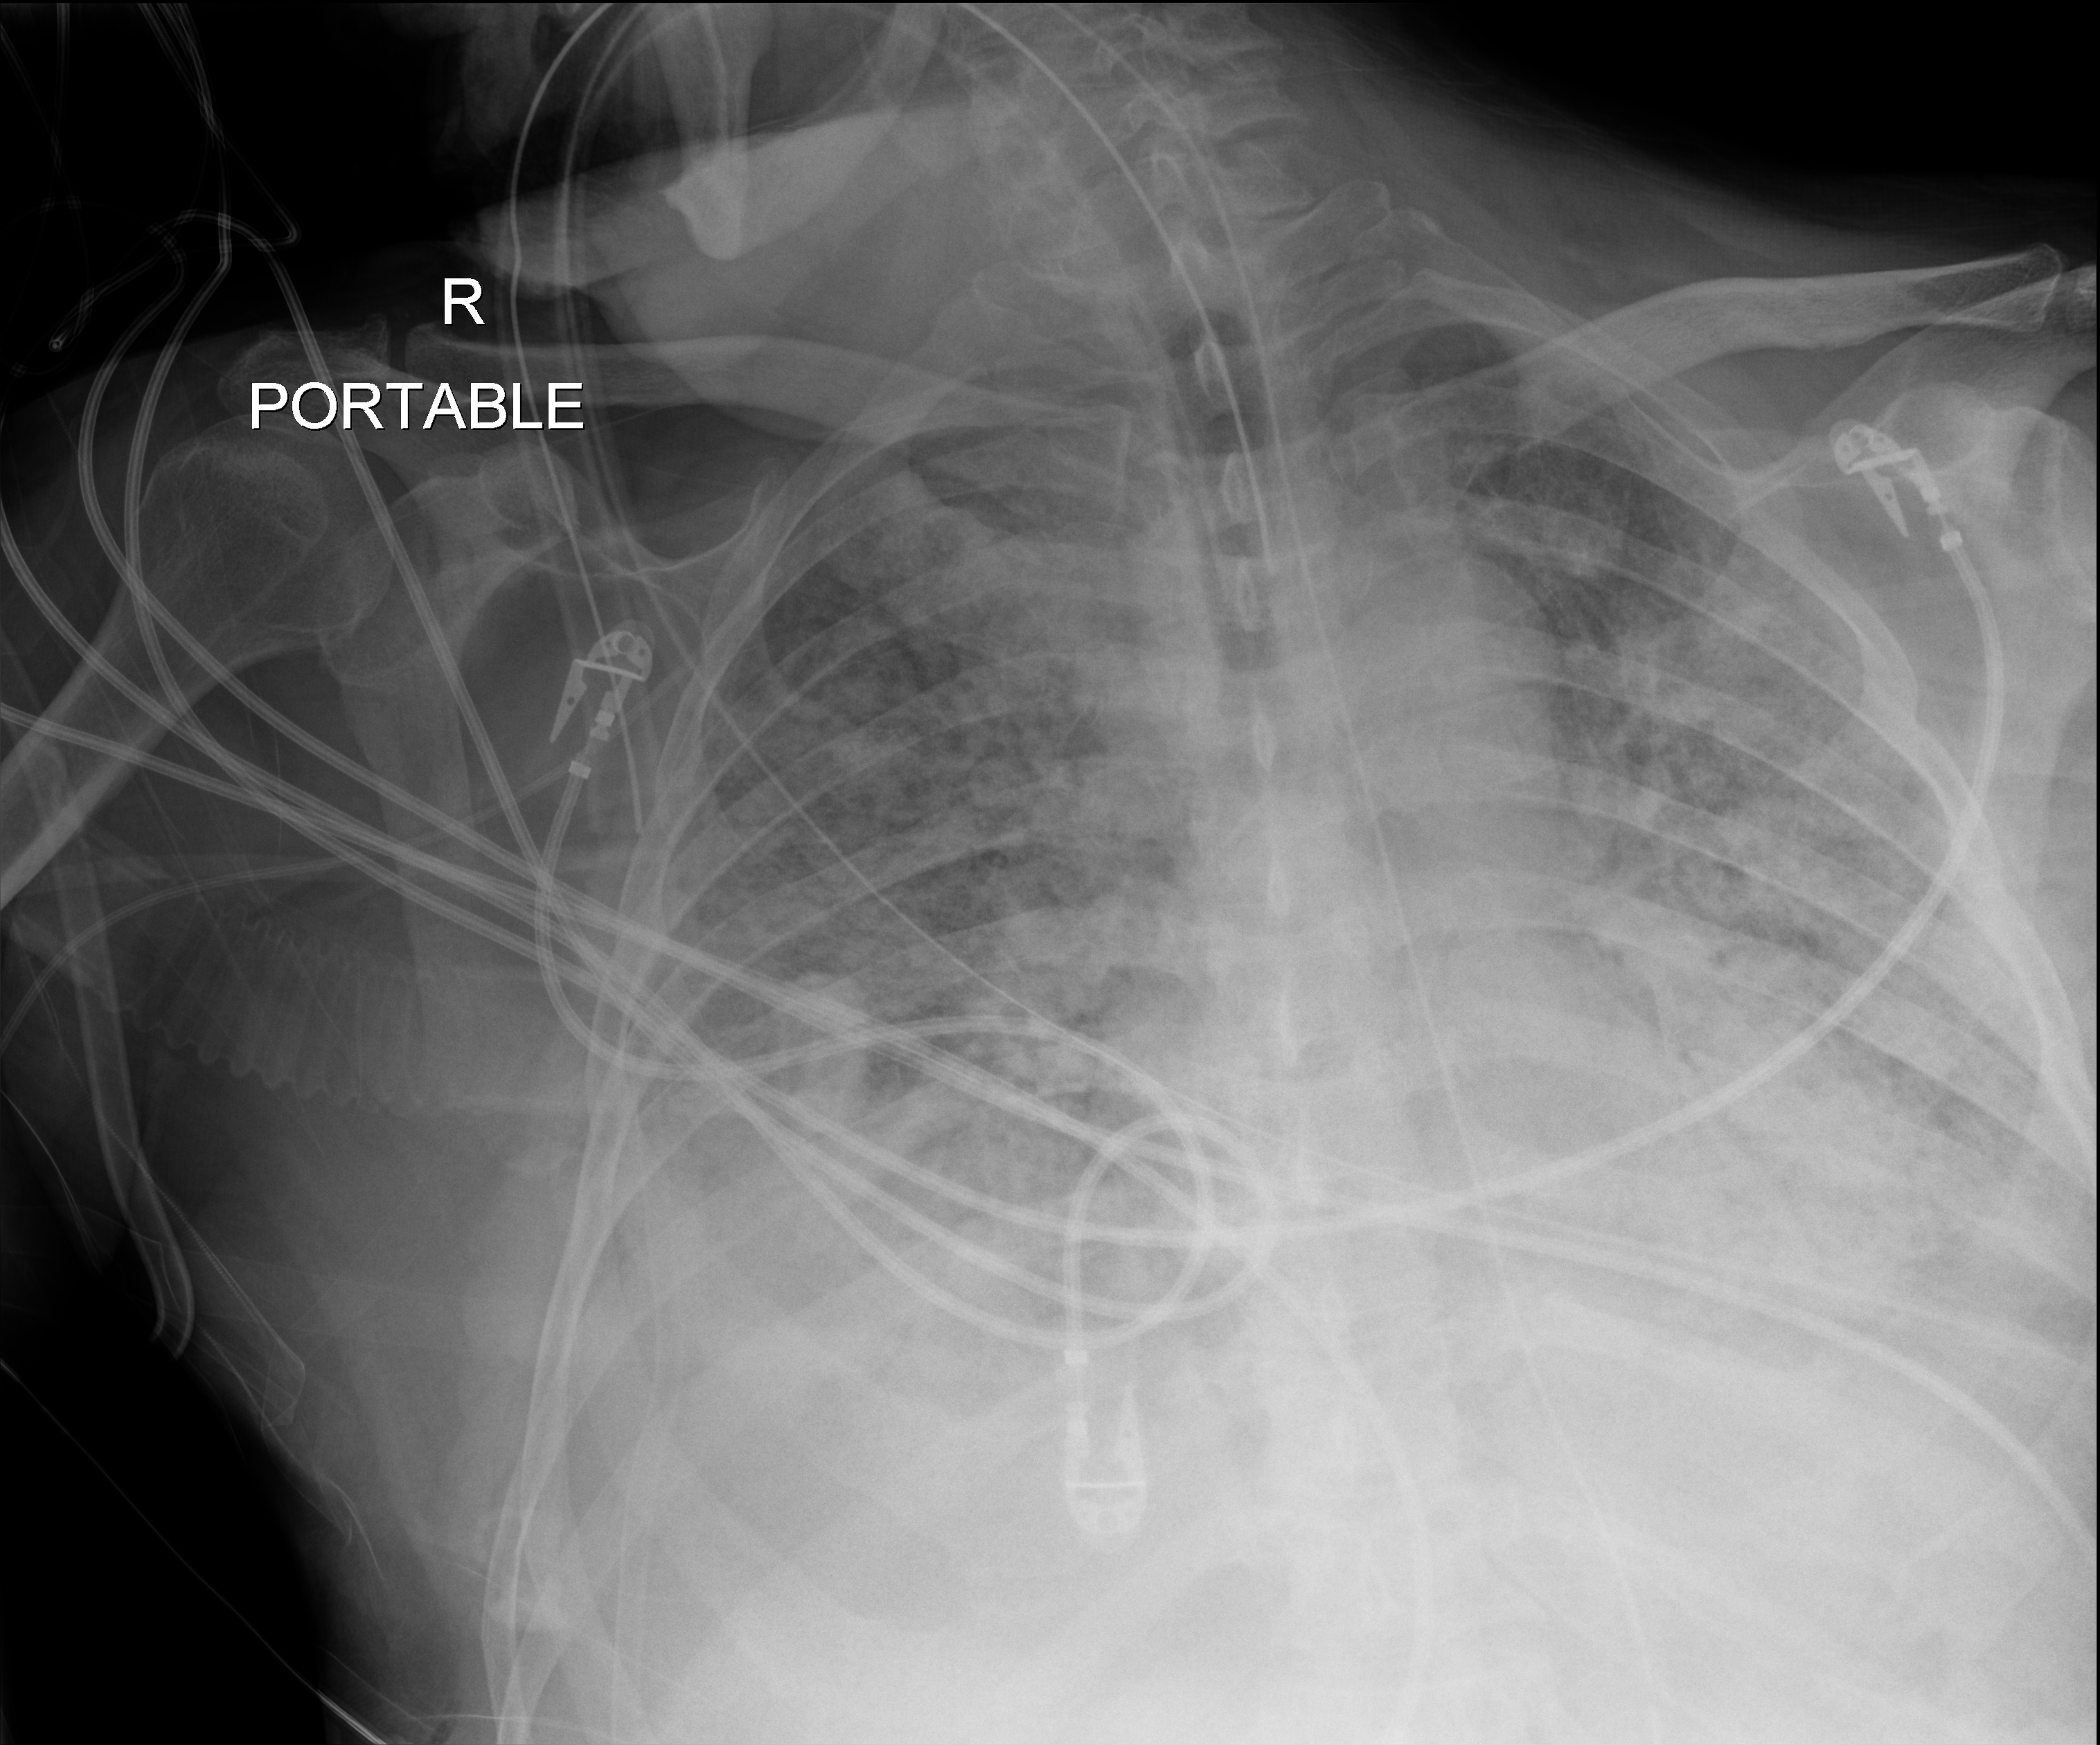
Portable chest radiograph; anteroposterior (AP) projection. Patient hospitalised with COVID-19; male, aged 60–74 years.
From the hospital-stay record, not from the radiograph (when in the stay this image was taken is not recorded):
- diabetes (admission record): yes